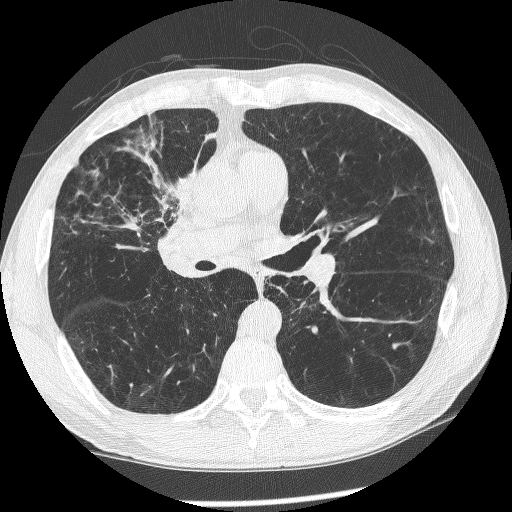
Chest CT (low-dose screening protocol), one axial image; baseline annual screen; lung window (W 1500 / L -600 HU); 1.25 mm slice thickness; lung (sharp) reconstruction kernel (BONE); 120 kVp. Male, age 60 years at enrolment. Current smoker at enrolment.
• Expert-annotated lung lesion, bounding box [x1, y1, x2, y2] px = [146, 176, 215, 270].
• Screening reader's record for this exam (one nodule recorded; not confirmed to be the boxed lesion): non-calcified nodule or mass ≥4 mm, right upper lobe, 12 × 8 mm, spiculated (stellate) margins, mixed attenuation.
• Official screen result: positive, change unspecified: nodule(s) >= 4 mm or enlarging nodule(s), mass(es), or other non-specific abnormalities suspicious for lung cancer.